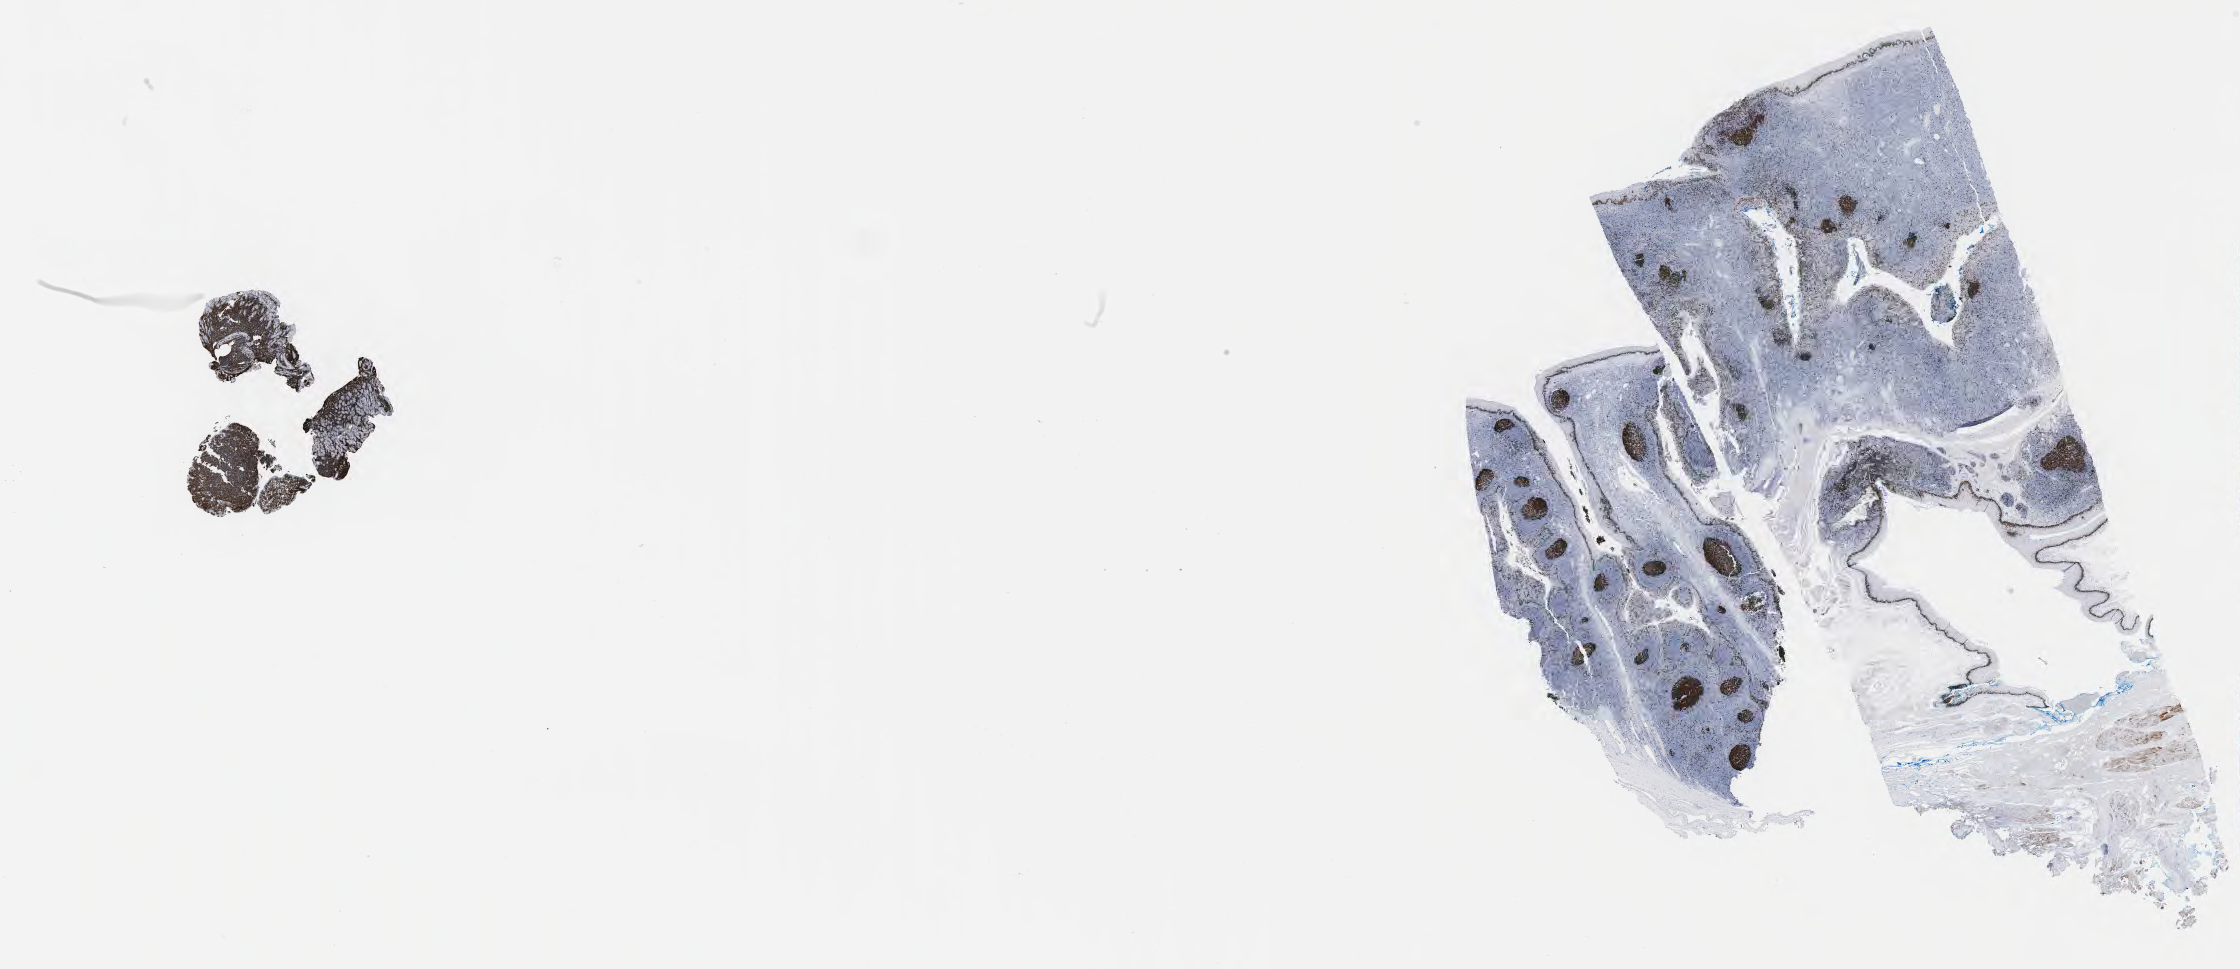
IHC for Ki-67, whole-slide image — whole scanned area (about 36.2 x 15.7 mm) shown as a low-resolution overview; specimen: tumor tissue. Female patient, aged 45.
• diagnosis: Burkitt lymphoma, NOS